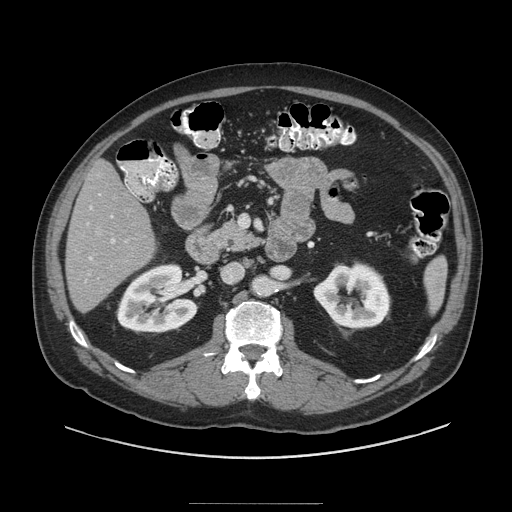
Contrast-enhanced abdominal CT (liver protocol), one axial slice. Slice 39 of 91 in the series (ordered by position). Soft-tissue window (W 400 / L 40 HU). 512 × 512 image matrix. Case-level facts recorded for this patient, not image findings: diagnosis: hepatocellular carcinoma (patient treated with transarterial chemoembolisation; whether this scan precedes or follows treatment is not stated here); TNM stage (as recorded): Stage-I; Child-Pugh class: A.
Annotated regions visible in this slice (semi-automatic segmentation, software-assisted and operator-edited):
- liver parenchyma outside the tumour (the mass and vessels are separate outlines, so this box may not span the whole liver): bounding box (x1, y1, x2, y2) in pixels: (66, 160, 154, 312)
- liver vessels: (85, 206, 115, 282)